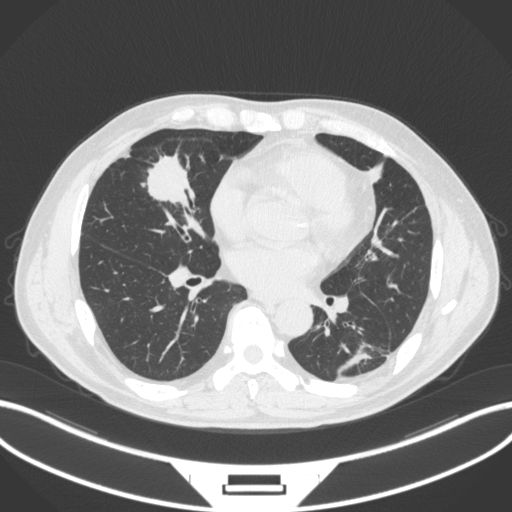
Chest CT, one axial slice. Slice 131 of 399 in the series (ordered by position). Reconstruction kernel B31f. Lung window (W 1500 / L -600 HU). 1 mm slice thickness. 512 × 512 image matrix, field of view 400 × 400 mm. Patient: male, 59 years. Case-level facts recorded for this patient, not image findings: clinical TNM (as recorded): T2a N1 M0.
Outlined on this slice (bounding box drawn by a radiologist):
- lung tumour (recorded histology: adenocarcinoma): bounding box (x1, y1, x2, y2) in pixels: (142, 147, 199, 209)